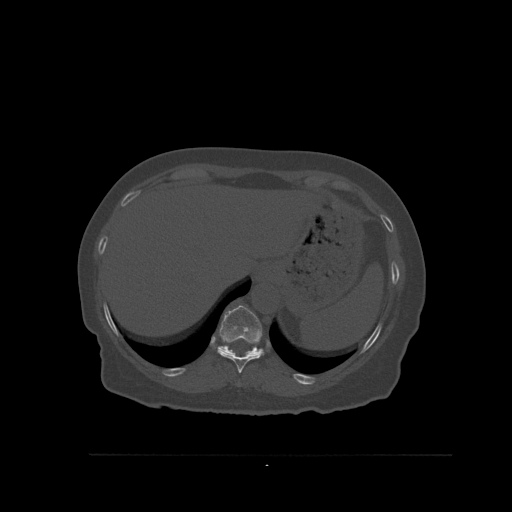
CT including the spine, one axial slice. Slice 314 of 527 in the series (ordered by position). Bone window (W 1800 / L 400 HU). 512 × 512 image matrix, field of view 470 × 470 mm. Female patient, age 73 years. From the clinical record (not read from this slice): primary cancer: breast; vertebrae with lytic lesions (as recorded): L2.
Structures marked on this image (semi-automatic segmentation, software-assisted and operator-edited):
- T10 vertebra: bounding box [x1, y1, x2, y2] px = [217, 347, 265, 373]
- T11 vertebra: [217, 305, 264, 357]